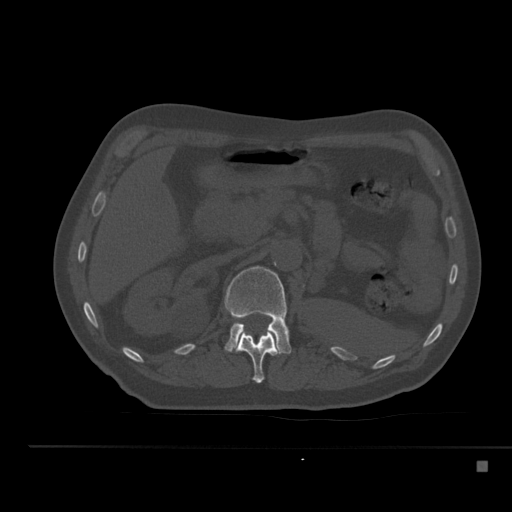
CT including the spine, one axial slice. Position 217 of 517 along the scan axis. Reconstruction kernel Br40s. 120 kVp. Bone window (W 1800 / L 400 HU). 1.5 mm slice thickness. 512 × 512 image matrix, field of view 408 × 408 mm. Patient: male, 70 years. Case-level facts recorded for this patient, not image findings: primary cancer: renal.
Outlined on this slice (semi-automatically segmented with operator editing):
- L1 vertebra: bounding box (x1, y1, x2, y2) in pixels: (224, 266, 291, 354)
- T12 vertebra: (235, 327, 279, 383)